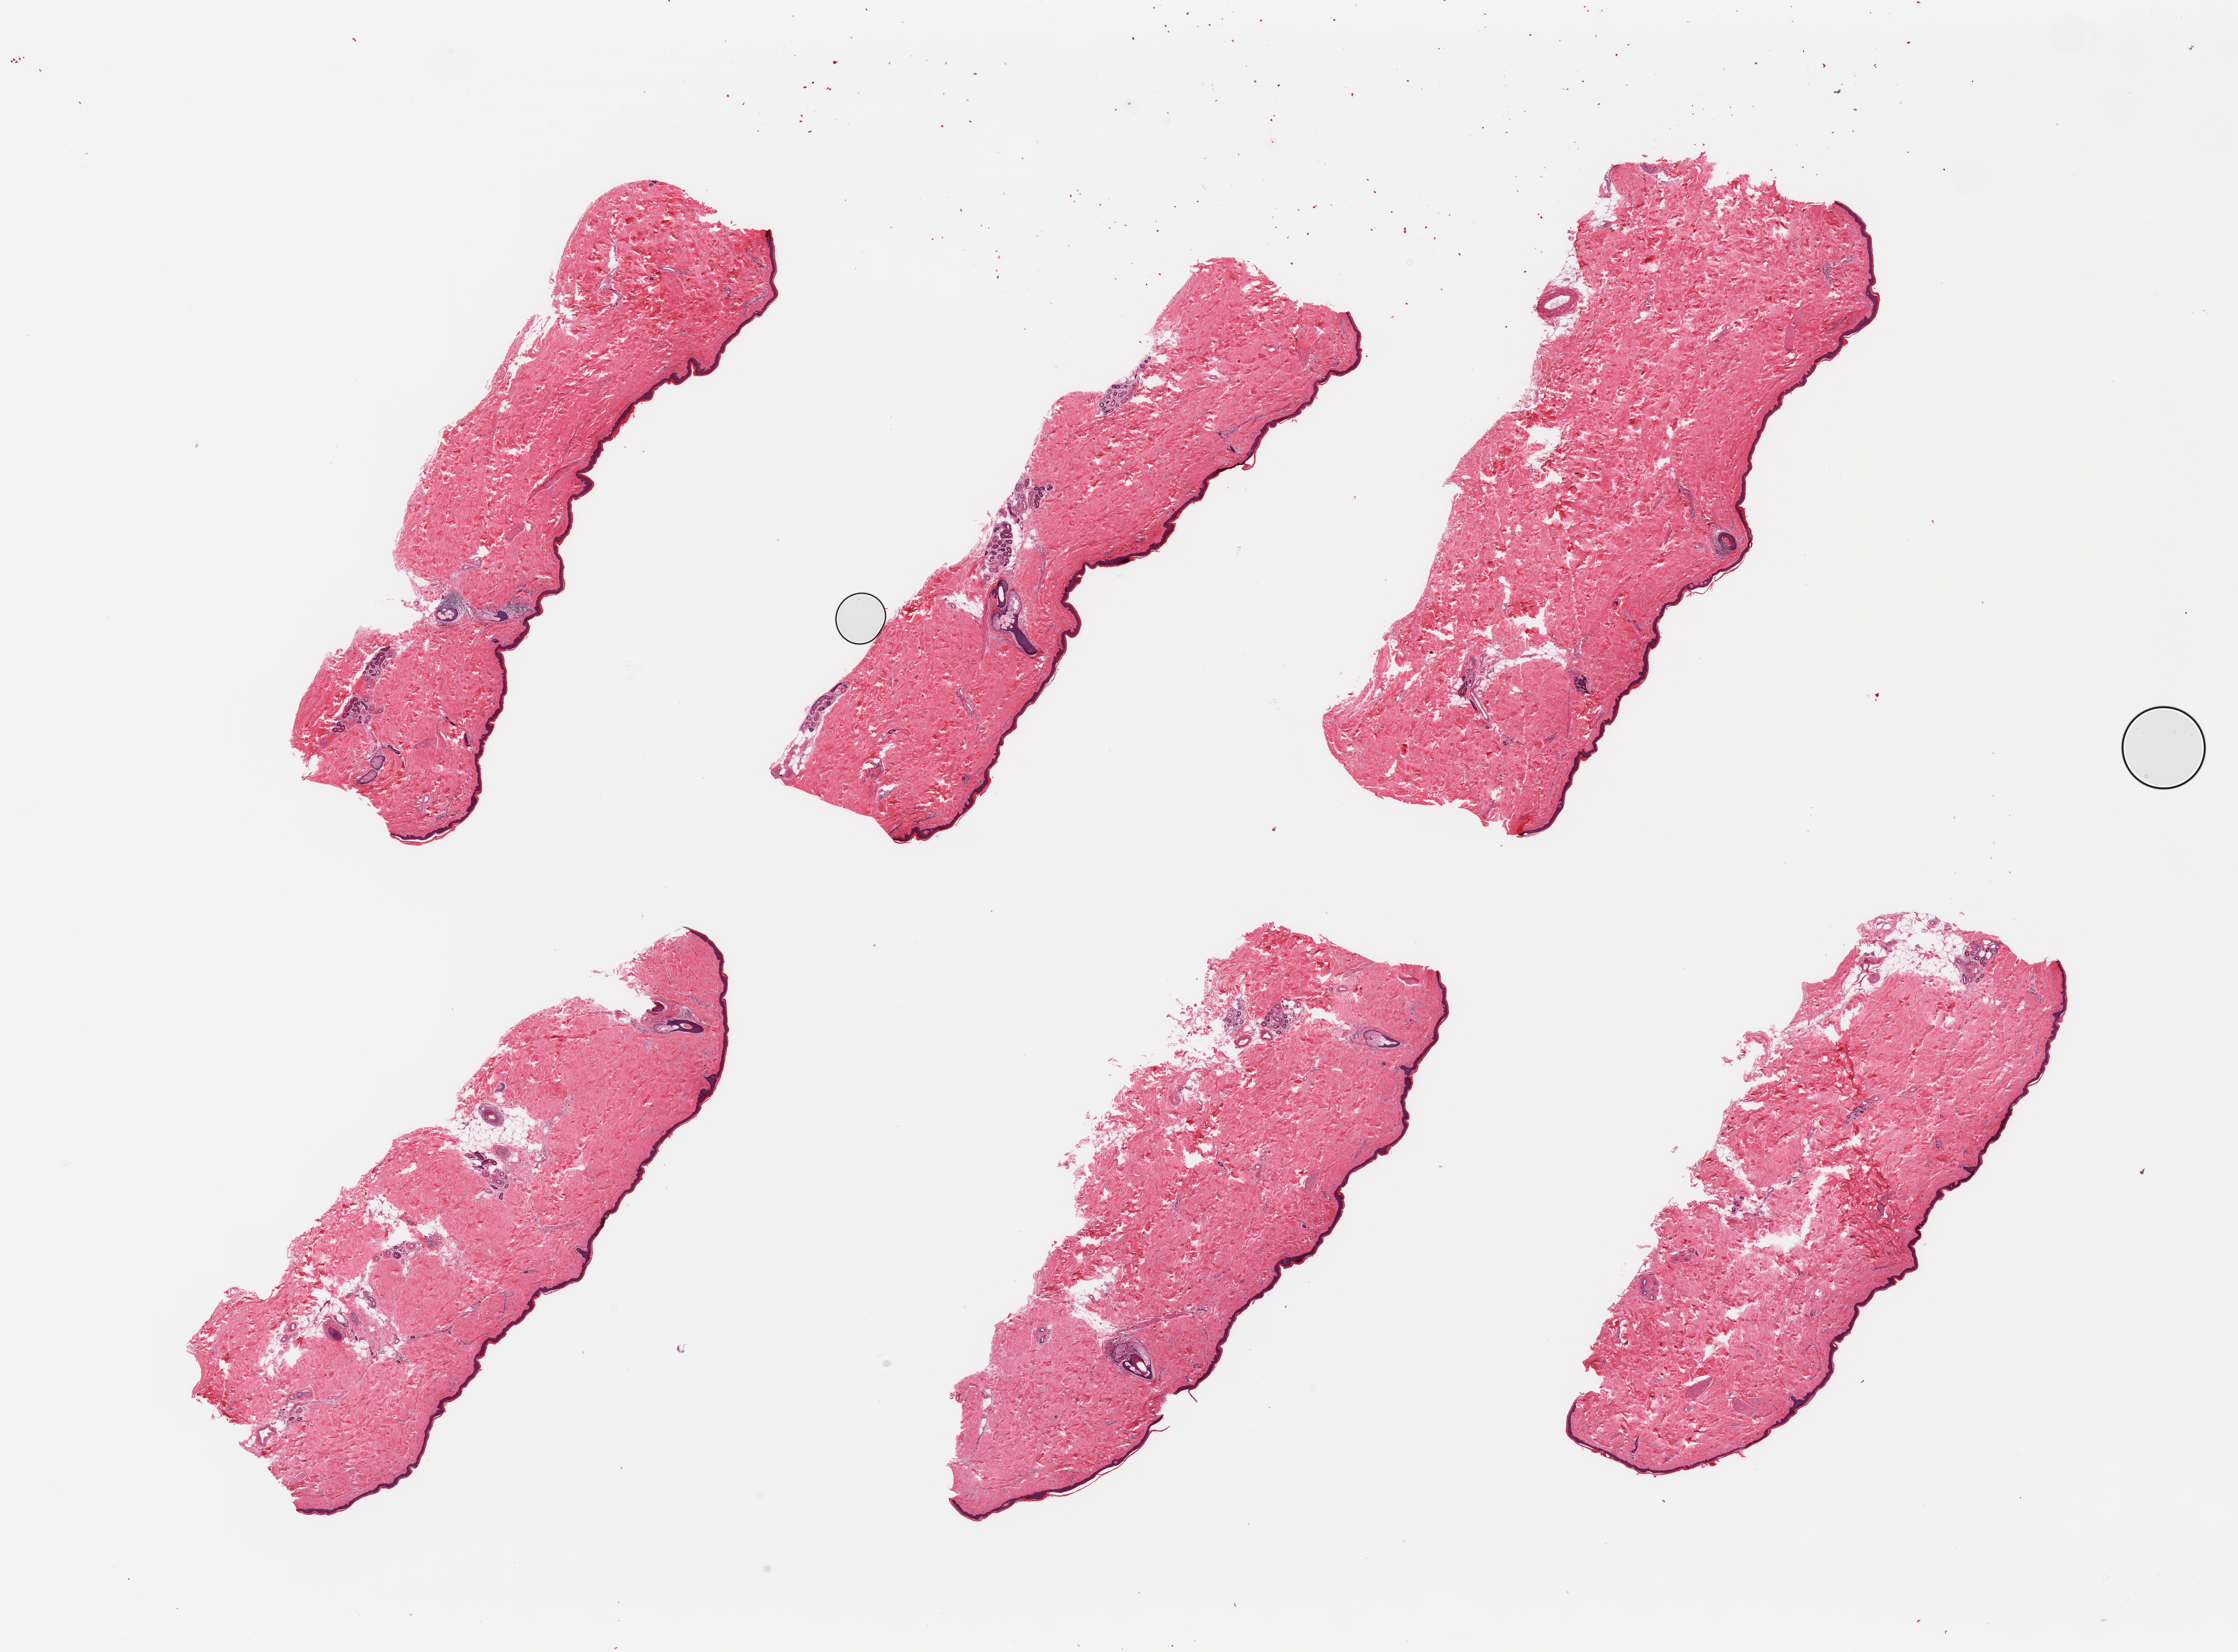
Whole-slide image, haematoxylin and eosin stain, shown as a low-resolution overview of the whole scanned area (about 29.5 x 21.8 mm, from a 20x scan). PAXgene-fixed paraffin-embedded (PFPE) section. Target tissue: skin of lower leg. Tissue donor sample. Male donor.
• pathologist's review note for this sample: 6 pieces; well trimmed with minimal internal/periadnexal fat, epidermis measures about 34 microns, few collections of lymphocytes